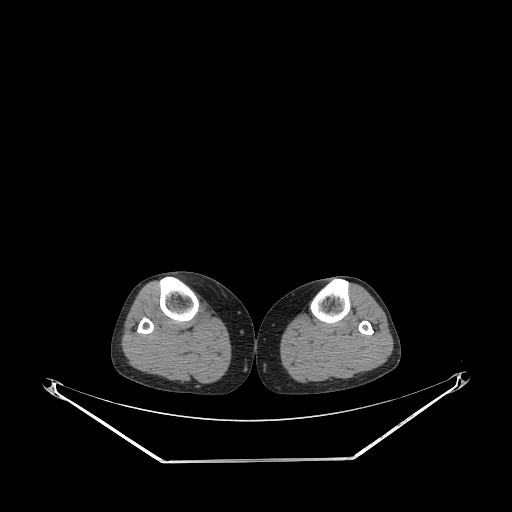
CT of an extremity soft-tissue mass (from a PET/CT study), one axial slice. Slice 155 of 267 in the series (ordered by position). 140 kVp. Soft-tissue window (W 400 / L 40 HU). 512 × 512 image matrix, field of view 500 × 500 mm. Female patient. From the clinical record (not read from this slice): histological type: undifferentiated – high grade; grade: high; site of the primary tumour: right thigh.
Outlined on this slice (expert contour drawn on MRI and transferred to this co-registered scan by the dataset authors):
- gross tumour volume (mass): bounding box <196,302,211,325> (left, top, right, bottom; pixels)